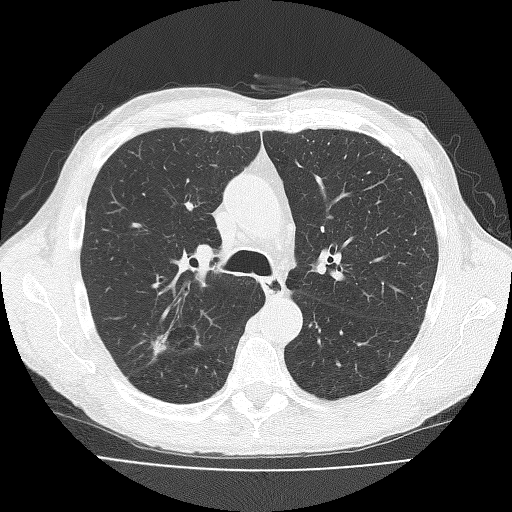
Axial slice from a low-dose chest CT screening exam; third screening round (two years after baseline); lung window (W 1500 / L -600 HU); lung (sharp) reconstruction kernel (FC51); slice 64 of 181 in the series; 512 × 512 image matrix. Male participant, aged 73 years at enrolment.
• Expert-annotated lung lesion, bounding box [x1, y1, x2, y2] px = [139, 318, 194, 377].
• Screening reader's record for this exam (one nodule recorded; not confirmed to be the boxed lesion): non-calcified nodule or mass ≥4 mm, right upper lobe, 11 × 10 mm, spiculated (stellate) margins, soft tissue attenuation, pre-existing on the prior screen: no.
• Official screen result: positive, other.
• Later outcome: lung cancer diagnosed 38 days after this screen — adenosquamous carcinoma, right upper lobe, well differentiated (G1), stage IA (AJCC 6th edition), 20 mm at pathology.